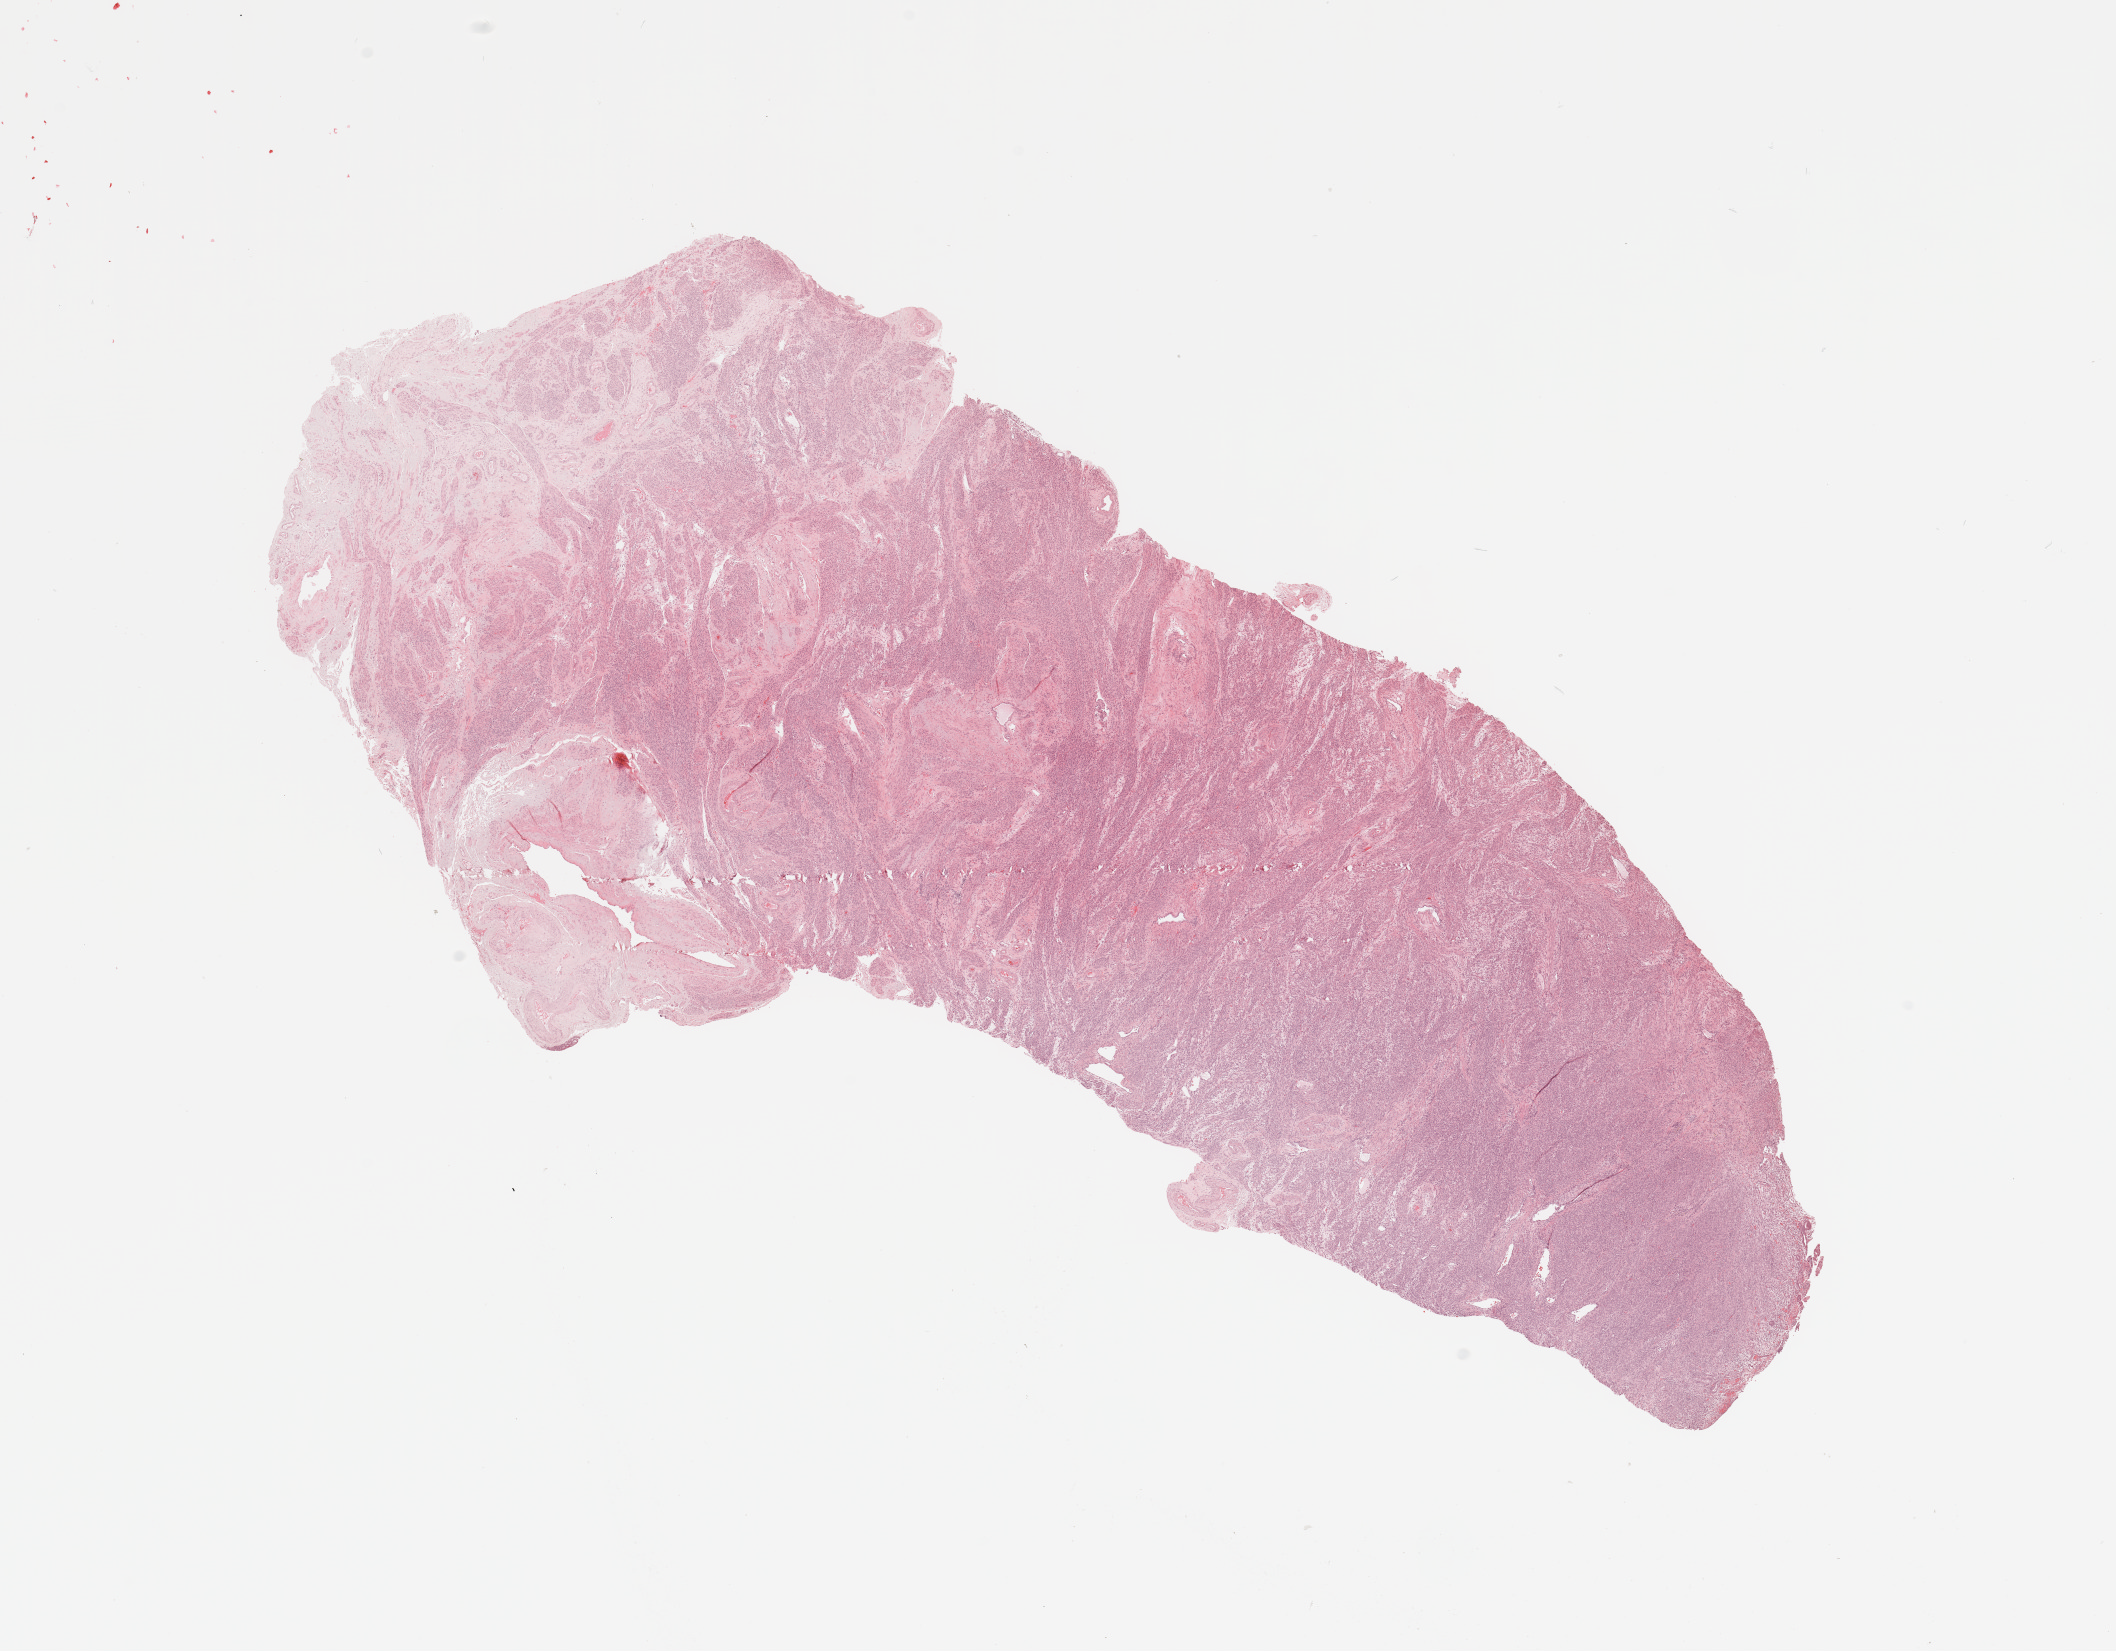
Digitized Hematoxylin and eosin (H&E) stained tissue section (whole slide) — shown as a low-resolution overview of the whole scanned area (about 16.7 x 13.1 mm, from a 20x scan), uterus, normal (non-tumour) tissue. Female, 86 y/o.
This section: normal (non-tumour) tissue from the same patient. Patient diagnosis: Endometrioid adenocarcinoma, NOS.